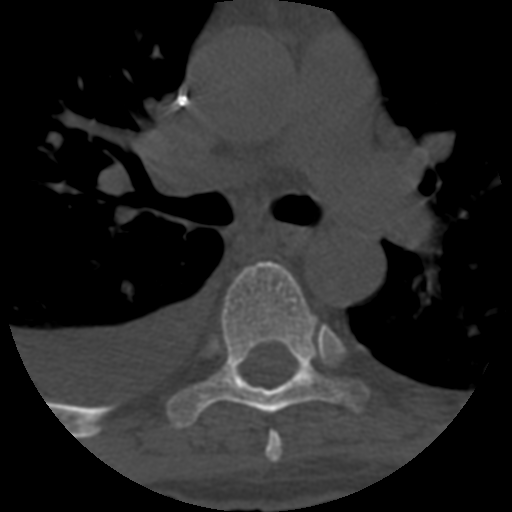
CT including the spine, one axial slice; slice 437 of 708 in the series (ordered by position); reconstruction kernel STANDARD; 120 kVp; one of 3 acquisitions stored at this slice position; bone window (W 1800 / L 400 HU); 1.25 mm slice thickness; 512 × 512 image matrix, field of view 160 × 160 mm. Patient age 55 years. From the clinical record (not read from this slice): primary cancer: colon; vertebrae with lytic lesions (as recorded): T12, L1, L5.
Structures marked on this image (semi-automatically segmented with operator editing):
- T5 vertebra: bounding box (x1, y1, x2, y2) in pixels: (265, 432, 282, 462)
- T6 vertebra: (167, 262, 371, 430)